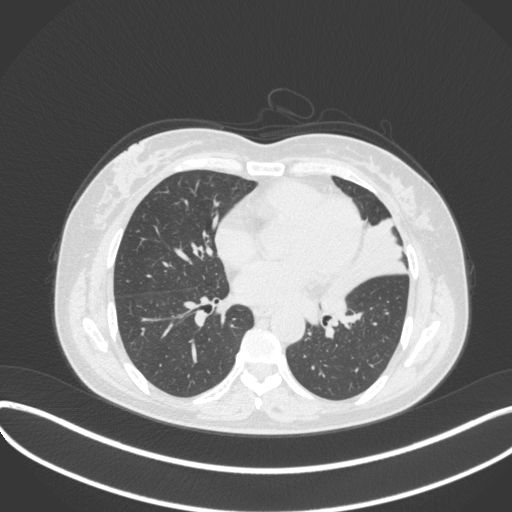
Chest CT, one axial slice; reconstruction kernel B31f; lung window (W 1500 / L -600 HU); 512 × 512 image matrix, field of view 400 × 400 mm. Female patient, age 54 years. From the clinical record (not read from this slice): clinical TNM (as recorded): T2a N1 M0.
Structures marked on this image (rectangle marked by the reading radiologist):
- lung tumour (recorded histology: small cell carcinoma): box from (x=313, y=274) to (x=355, y=322) px